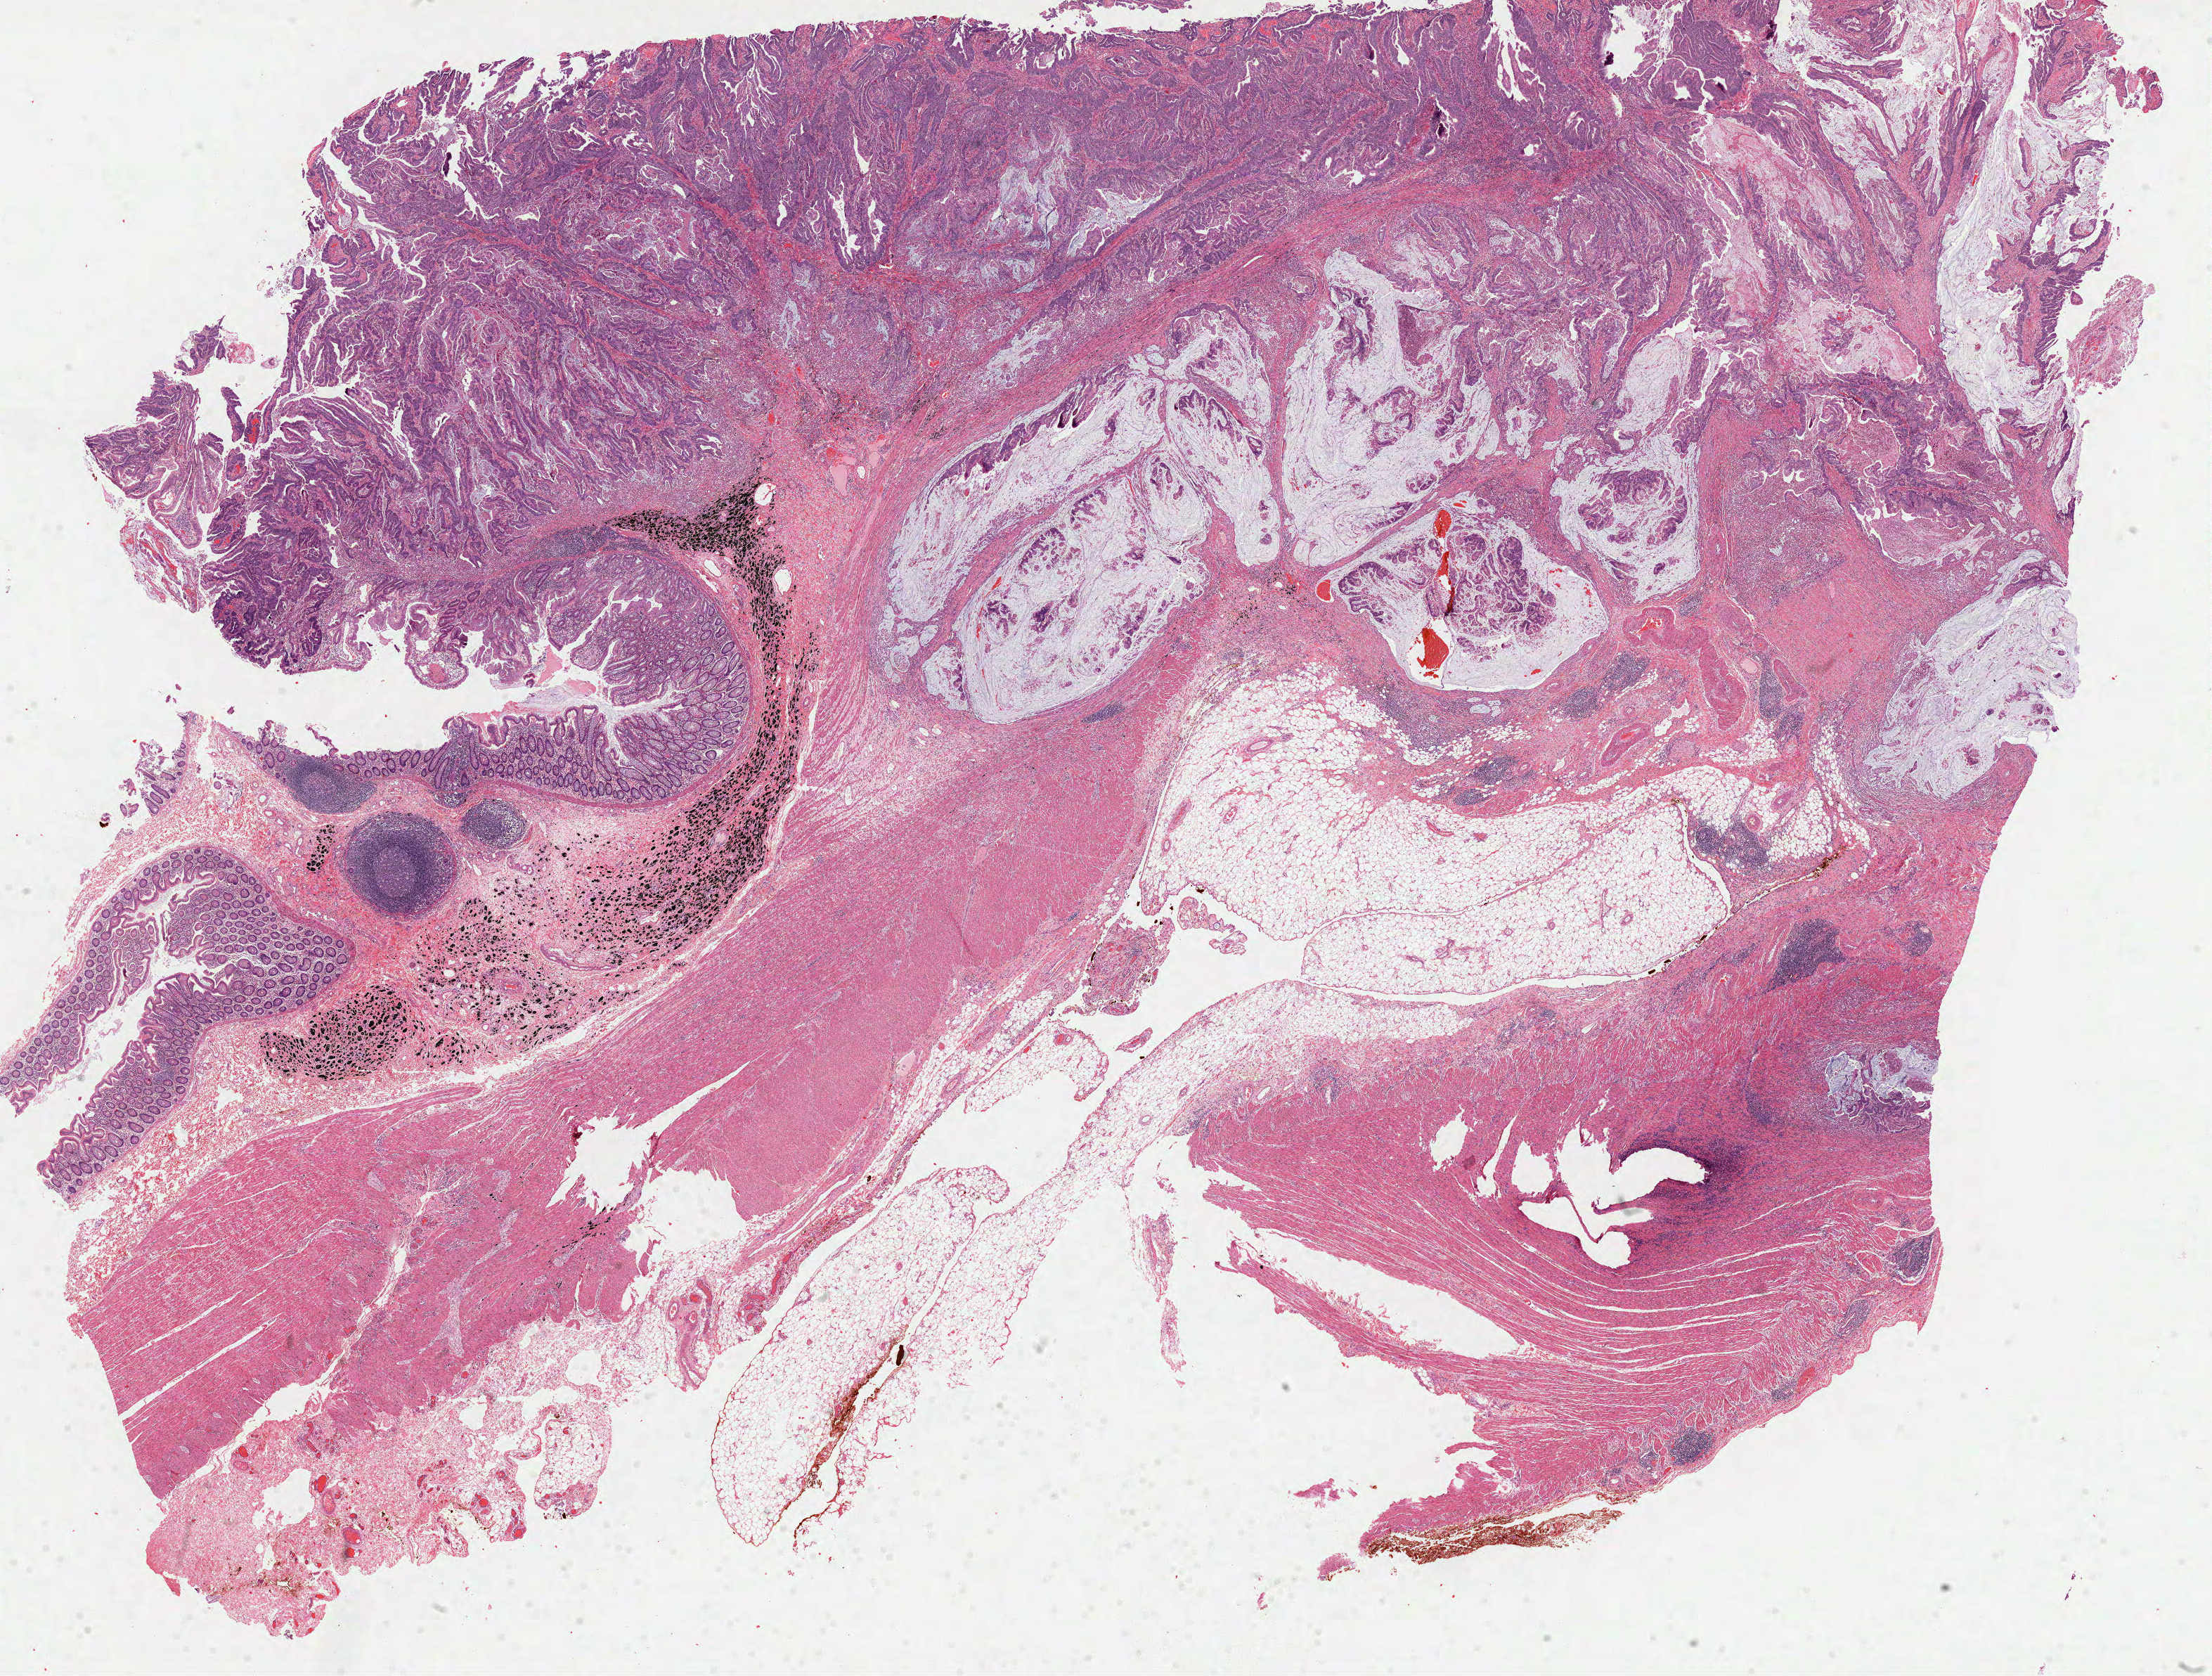
Hematoxylin and eosin (H&E) stained whole-slide image — a low-resolution overview of the entire scanned area, about 25.4 x 19.2 mm (from a 40x scan); FFPE section; colon, primary tumour sample. Female, age 58 years at initial diagnosis.
- TNM: T3 N0 MX
- AJCC pathologic stage: IIA (6th edition)
- diagnosis: Adenocarcinoma, NOS (ascending colon)